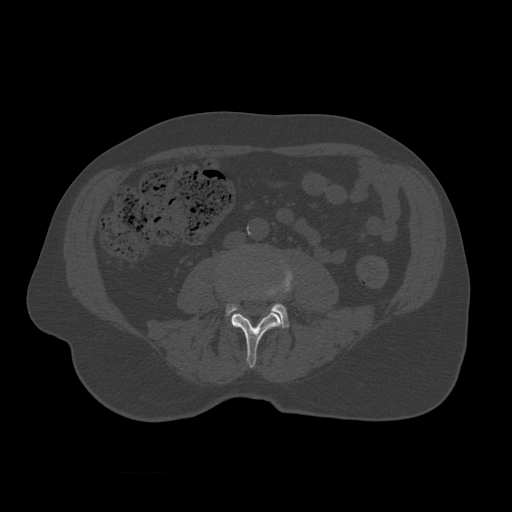
CT including the spine, one axial slice. Slice 291 of 450 in the series (ordered by position). Reconstruction kernel STANDARD. Bone window (W 1800 / L 400 HU). 512 × 512 image matrix, field of view 405 × 405 mm. Patient age 75 years. Case-level facts recorded for this patient, not image findings: primary cancer: prostate.
Annotated regions visible in this slice (semi-automatic segmentation, software-assisted and operator-edited):
- L3 vertebra: bounding box [x1, y1, x2, y2] px = [220, 280, 282, 368]
- L4 vertebra: [226, 264, 296, 329]